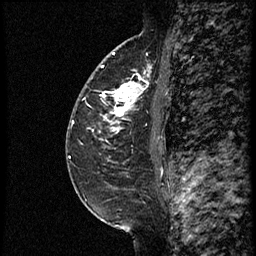
Breast MRI (dynamic contrast-enhanced), one sagittal slice; position 38 of 60 along the scan axis; dynamic contrast-enhanced study with each time point stored as its own series, time point 2 of 3 at this slice position (early post-contrast, ordered by acquisition time); 1.5 T; TE 4.2 ms, TR 18.9 ms; 2 mm slice thickness; 256 × 256 image matrix. Female patient. Case-level facts recorded for this patient, not image findings: setting: breast cancer imaged before/during neoadjuvant chemotherapy; receptor status: HER2-positive.
Outlined on this slice (semi-automatic segmentation, software-assisted and operator-edited):
- analysis volume of interest (the breast-tissue region the enhancement analysis was run in; not a lesion): box from (x=92, y=64) to (x=161, y=147) px
- tumour enhancement mask (voxels above the 100 % enhancement threshold inside the analysis volume of interest): (x=104, y=73)–(x=160, y=140)